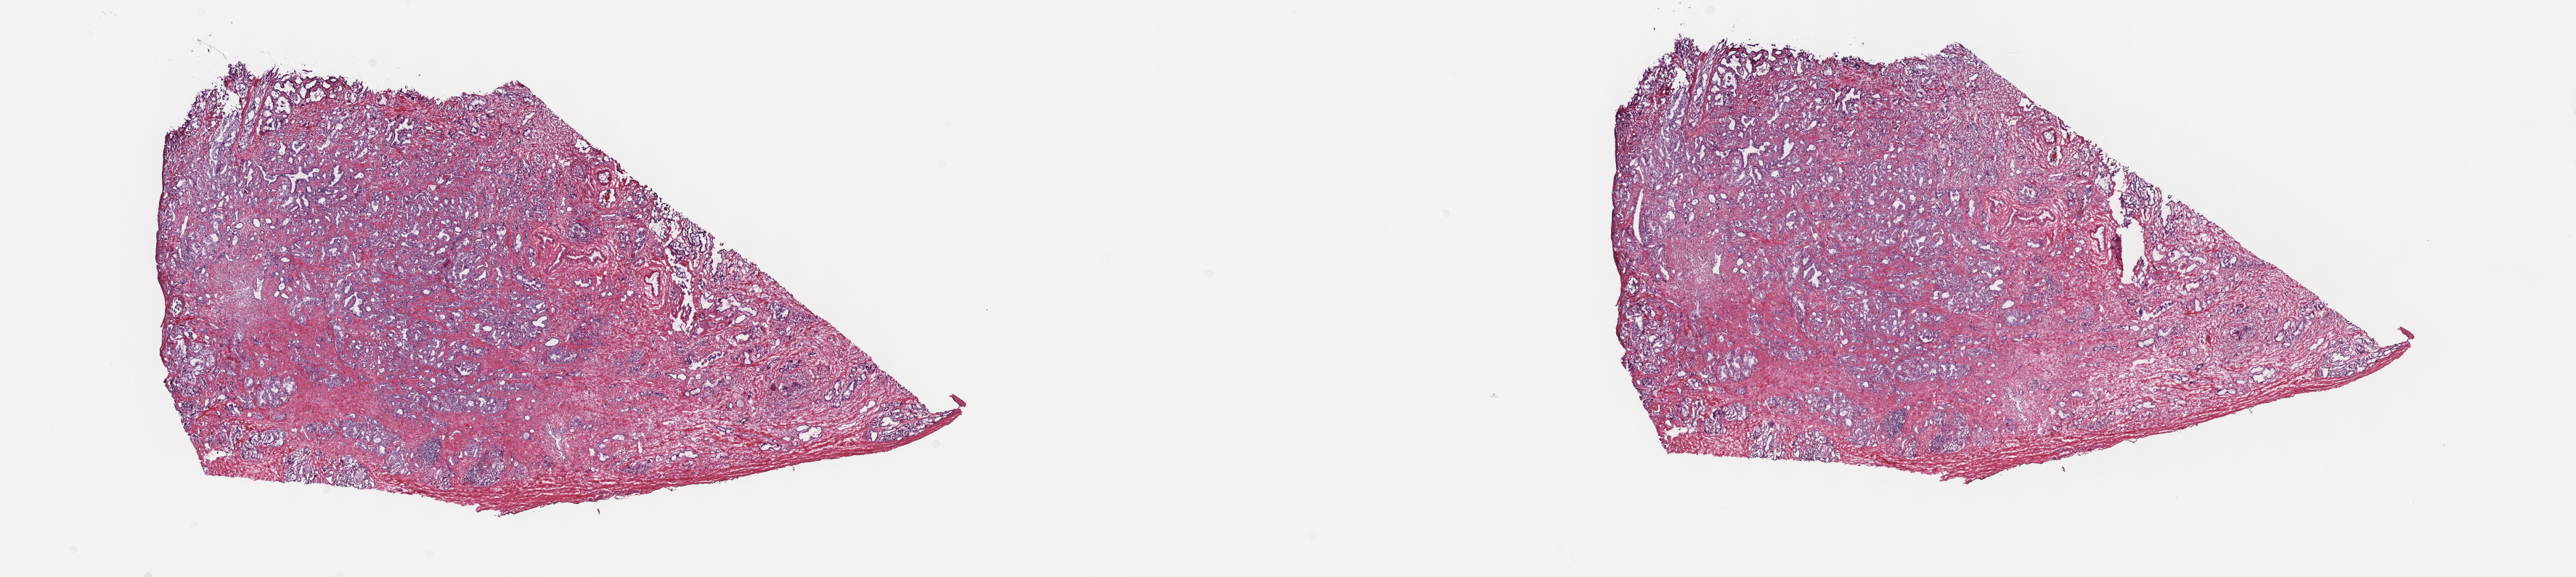
H&E-stained whole-slide image, a low-resolution overview of the entire scanned area, about 28.7 x 6.4 mm (slide scanned at 40x). Frozen section from the top of the tissue portion. Primary tumour sample from the prostate. Male patient; age at initial diagnosis 47 years. Gleason score: 8 (4+4). Composition of this section per pathologist review: tumour cells 50%, tumour nuclei 60%, normal cells 30%, stromal cells 20%, necrosis 0%. Inflammatory infiltration, as recorded: lymphocyte infiltration 0%, monocyte infiltration 0%, neutrophil infiltration 0%.
Laterality: bilateral. Diagnosis: Adenocarcinoma, NOS (prostate gland). Lymph nodes positive (case pathology): 1 of 10 examined.